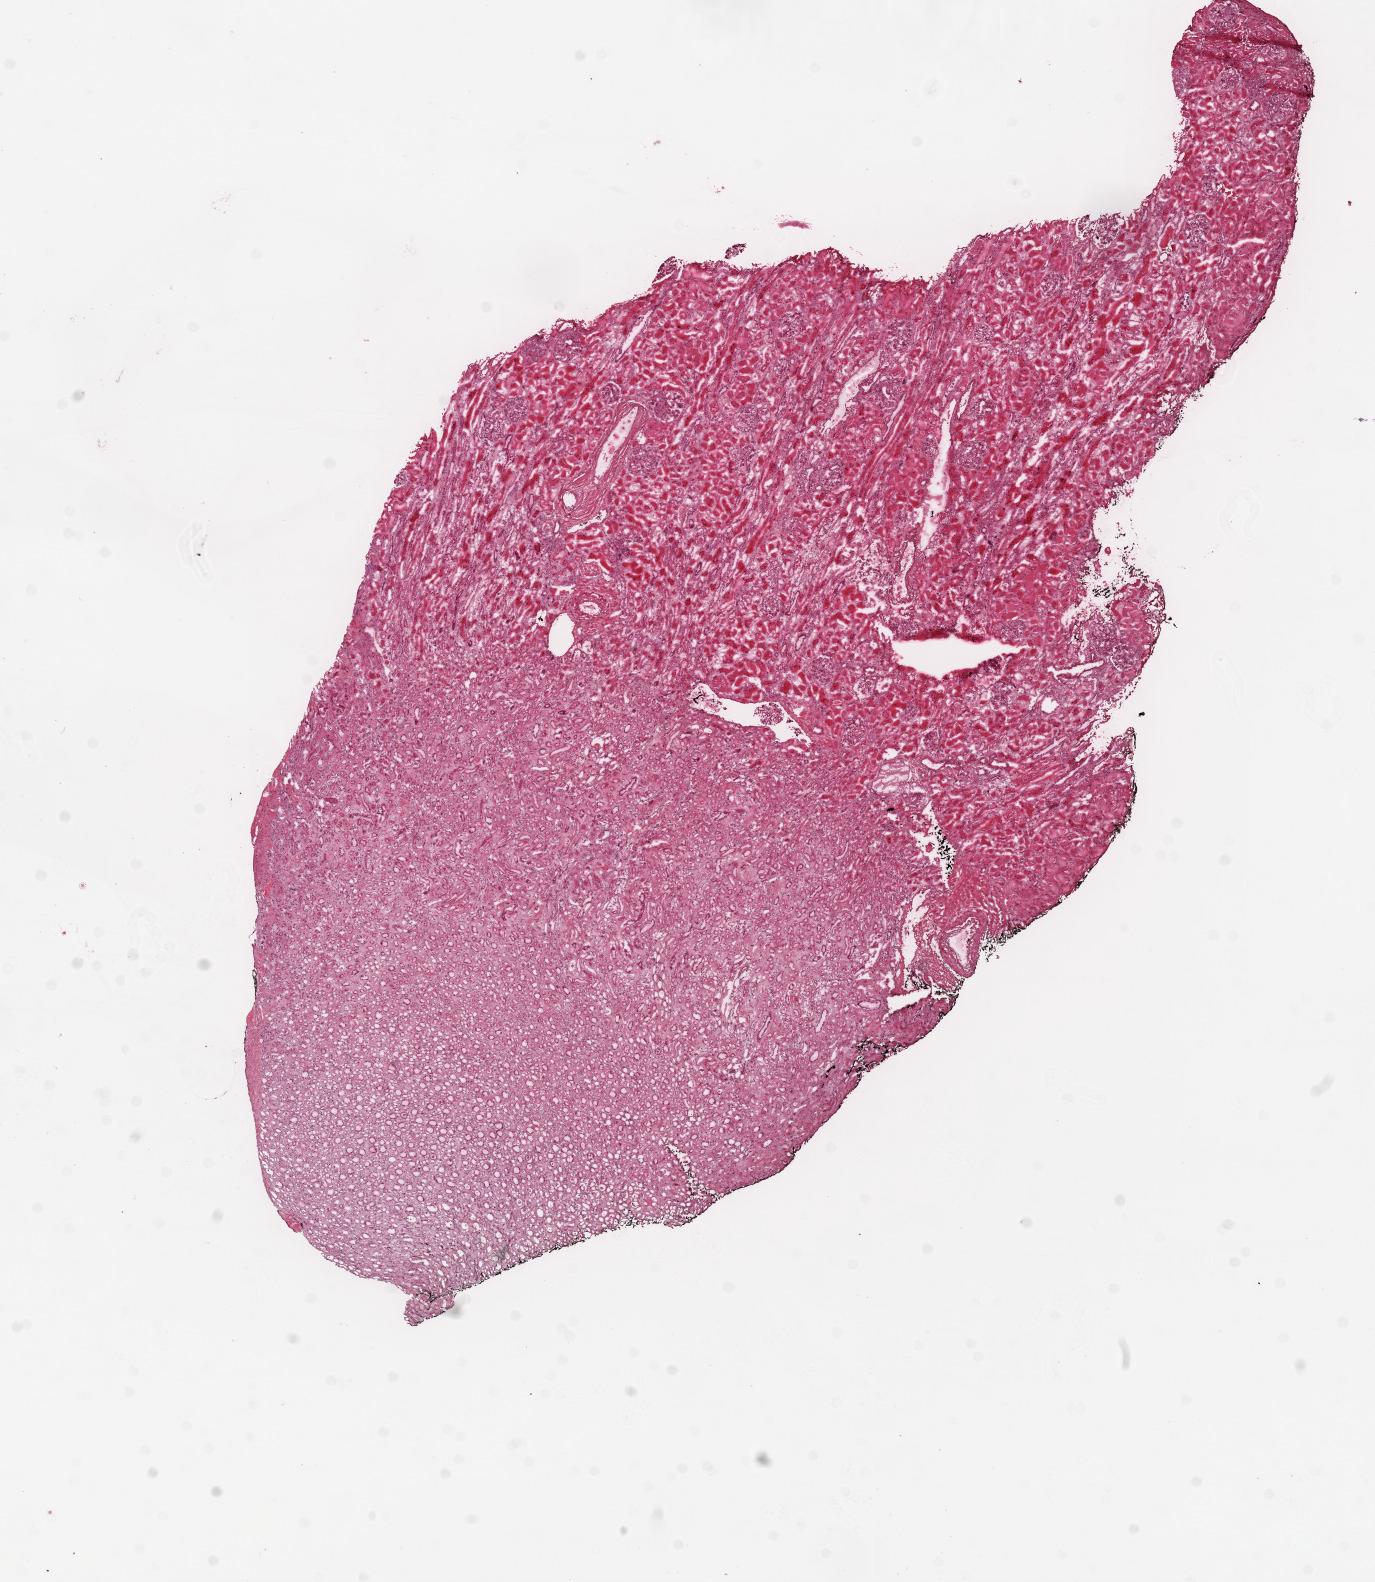
Whole-slide histology image, H&E-stained, shown as a low-resolution overview of the whole scanned area (about 11.0 x 12.7 mm). Frozen section from the top of the tissue portion. Solid tissue normal (non-tumour tissue) sample from the kidney. Male patient; age at initial diagnosis 75 years.
This section: solid tissue normal (non-tumour) sample from the same patient. Patient diagnosis: Clear cell adenocarcinoma, NOS.